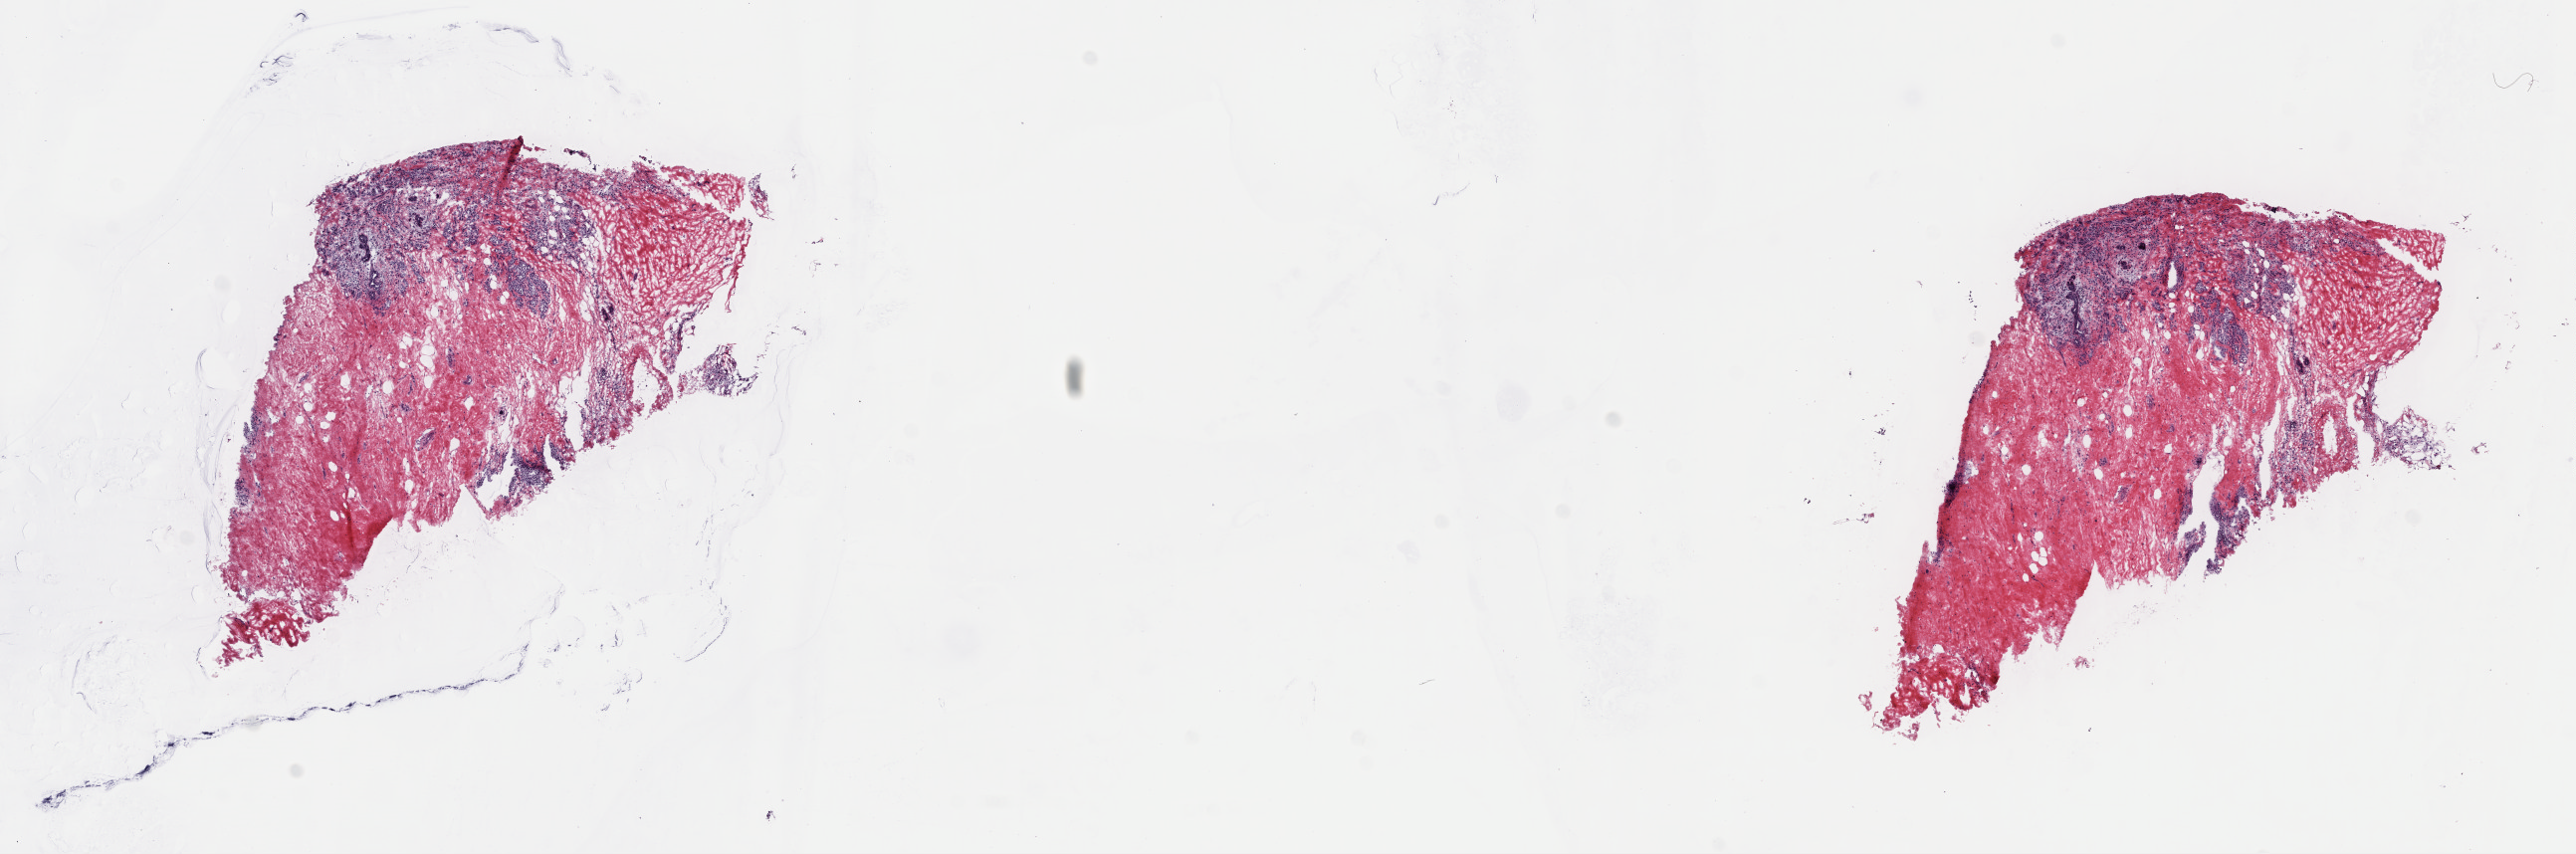
Whole-slide histology image, H&E-stained — a low-resolution overview of the entire scanned area, about 20.3 x 6.7 mm. Frozen section from the top of the tissue portion. Sample: primary tumour, breast. Female patient; age at initial diagnosis 62 years. Composition of this section per pathologist review: tumour cells 23%, tumour nuclei 60%, normal cells 2%, stromal cells 73%, necrosis 2%. Infiltration values recorded for this section: lymphocyte infiltration 1%, monocyte infiltration 0%, neutrophil infiltration 0%.
Diagnosis: Lobular carcinoma, NOS. AJCC pathologic stage: IIB (7th edition).